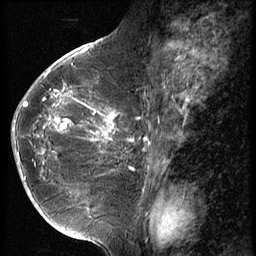
Breast MRI (dynamic contrast-enhanced), one sagittal slice. Slice 29 of 56 in the series (ordered by position). 3 images stored at this slice position (order not interpretable as contrast timing). 1.5 T. TE 4.2 ms, TR 9 ms. 2.5 mm slice thickness. 256 × 256 image matrix, field of view 180 × 180 mm. Female patient, age 49 years. From the clinical record (not read from this slice): setting: breast cancer imaged before/during neoadjuvant chemotherapy; receptor status: HER2-positive.
Outlined on this slice (semi-automatic segmentation, software-assisted and operator-edited):
- analysis volume of interest (the breast-tissue region the enhancement analysis was run in; not a lesion): box from (x=13, y=79) to (x=126, y=203) px
- tumour enhancement mask (voxels above the 140 % enhancement threshold inside the analysis volume of interest): (x=13, y=92)–(x=120, y=174)